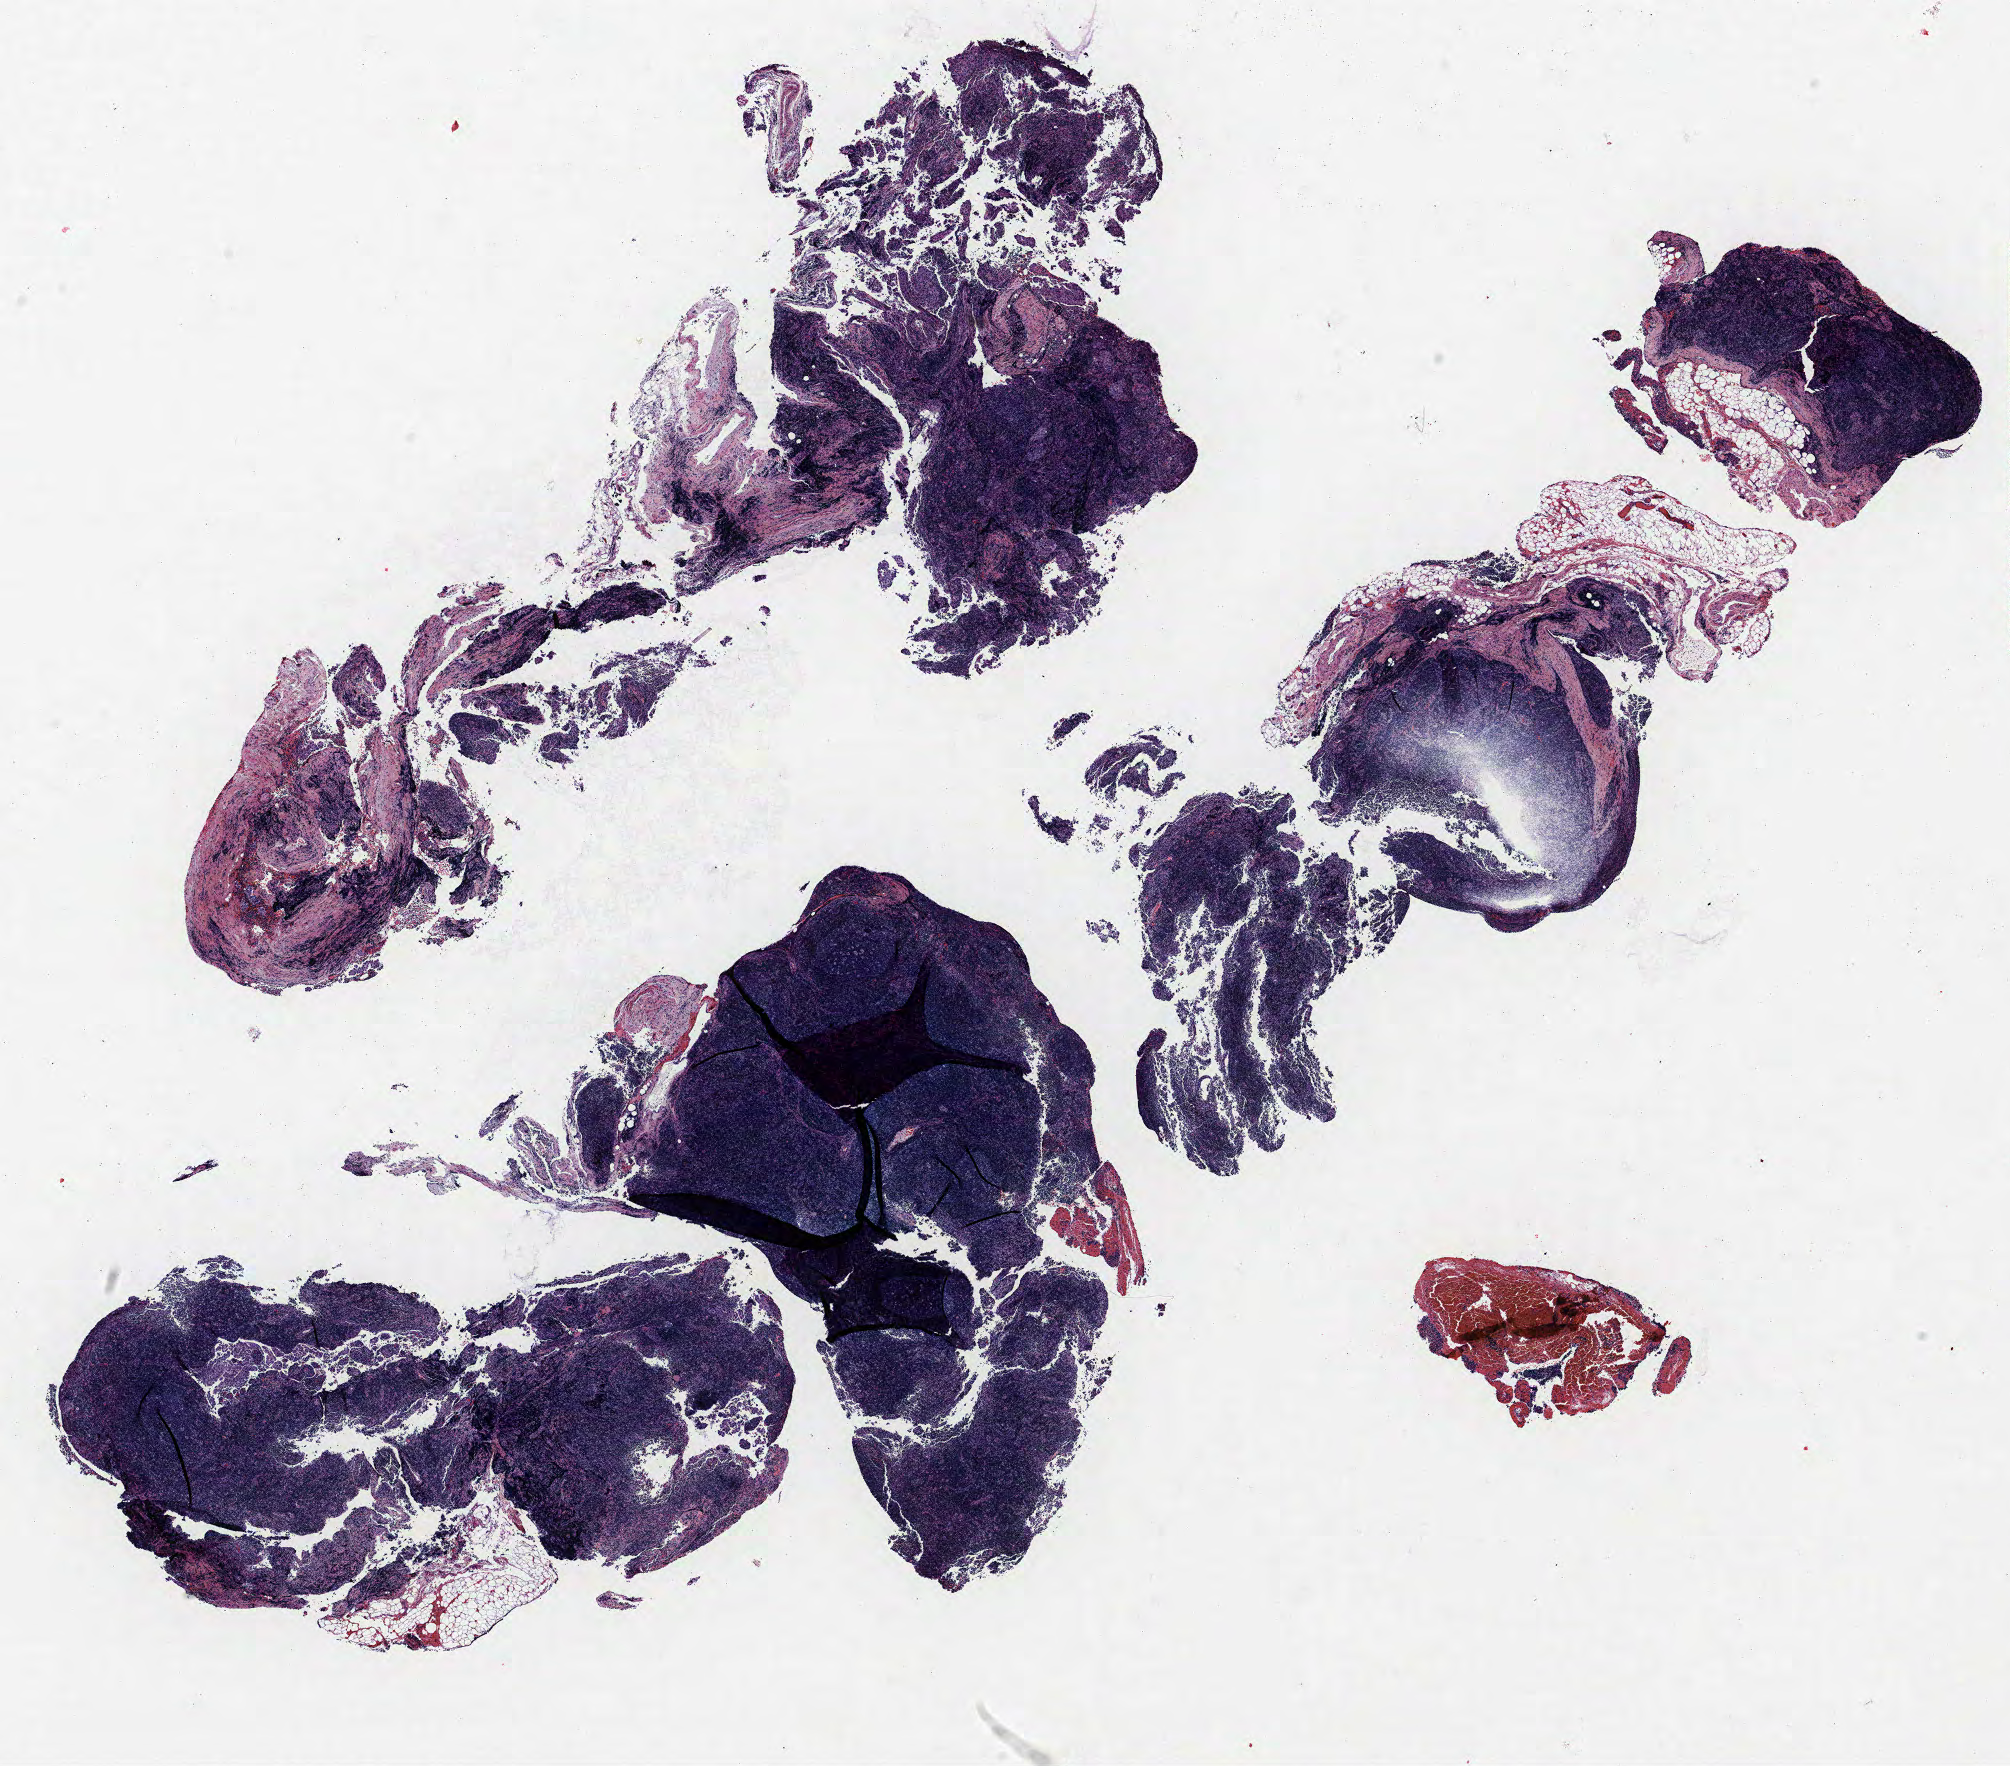
Whole-slide histology image, H&E-stained — low-resolution overview of the scanned area, about 16.1 x 14.1 mm (acquisition: 40x scan), formalin-fixed paraffin-embedded (FFPE) section, lung tissue. Female, age 62 at enrolment. Former smoker at enrolment. Grade: cannot be assessed (GX).
- stage (AJCC 6th edition): IIIB
- primary tumour location (clinical record): left lower lobe
- participant's lung-cancer diagnosis: Squamous cell carcinoma, NOS
- tumour size (pathology): 31 mm